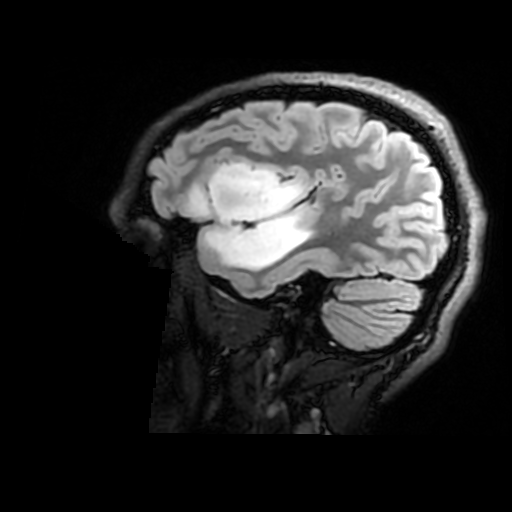
Brain MRI from a brain-tumour surgery series, one sagittal slice. Position 130 of 176 along the scan axis. T2 FLAIR. 1 mm slice thickness. 512 × 512 image matrix, field of view 240 × 240 mm. From the clinical record (not read from this slice): histopathology: Astrocytoma; WHO grade: 2; IDH mutation: yes; tumour location: Right Insular.
Annotated regions visible in this slice (expert manual segmentation):
- tumour: box from (x=192, y=162) to (x=311, y=272) px